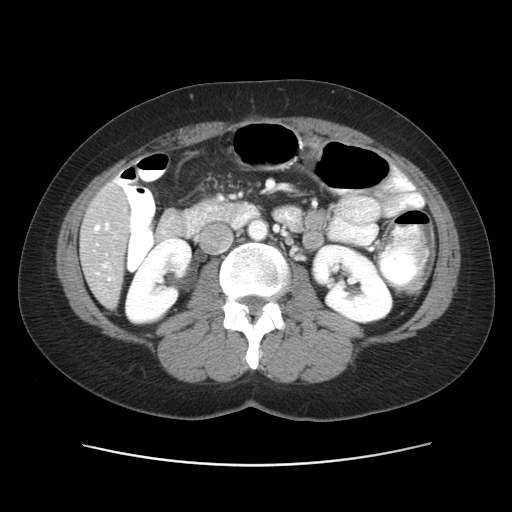
Contrast-enhanced abdominal CT, one axial slice; 120 kVp; intravenous contrast given; soft-tissue window (W 400 / L 40 HU); 5 mm slice thickness; 512 × 512 image matrix, field of view 362 × 362 mm. Female patient, age 48 years. From the clinical record (not read from this slice): diagnosis: colorectal cancer liver metastases, imaged before liver resection; multiple liver metastases: yes; largest metastasis: 4.5 cm; disease in both lobes: yes.
Structures marked on this image (manually delineated by an expert):
- hepatic veins: box from (x=94, y=225) to (x=111, y=280) px
- liver: (x=82, y=184)–(x=129, y=306)
- portal vein (with intrahepatic branches): (x=104, y=224)–(x=108, y=267)